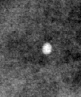
Crop from a digitized film mammogram around one marked abnormality, right breast, CC view.
- Marked abnormality: calcifications, morphology round and regular / lucent center; BI-RADS assessment category 2; subtlety rating 4 on a 1 (subtle) to 5 (obvious) scale; benign without callback (not worked up further).